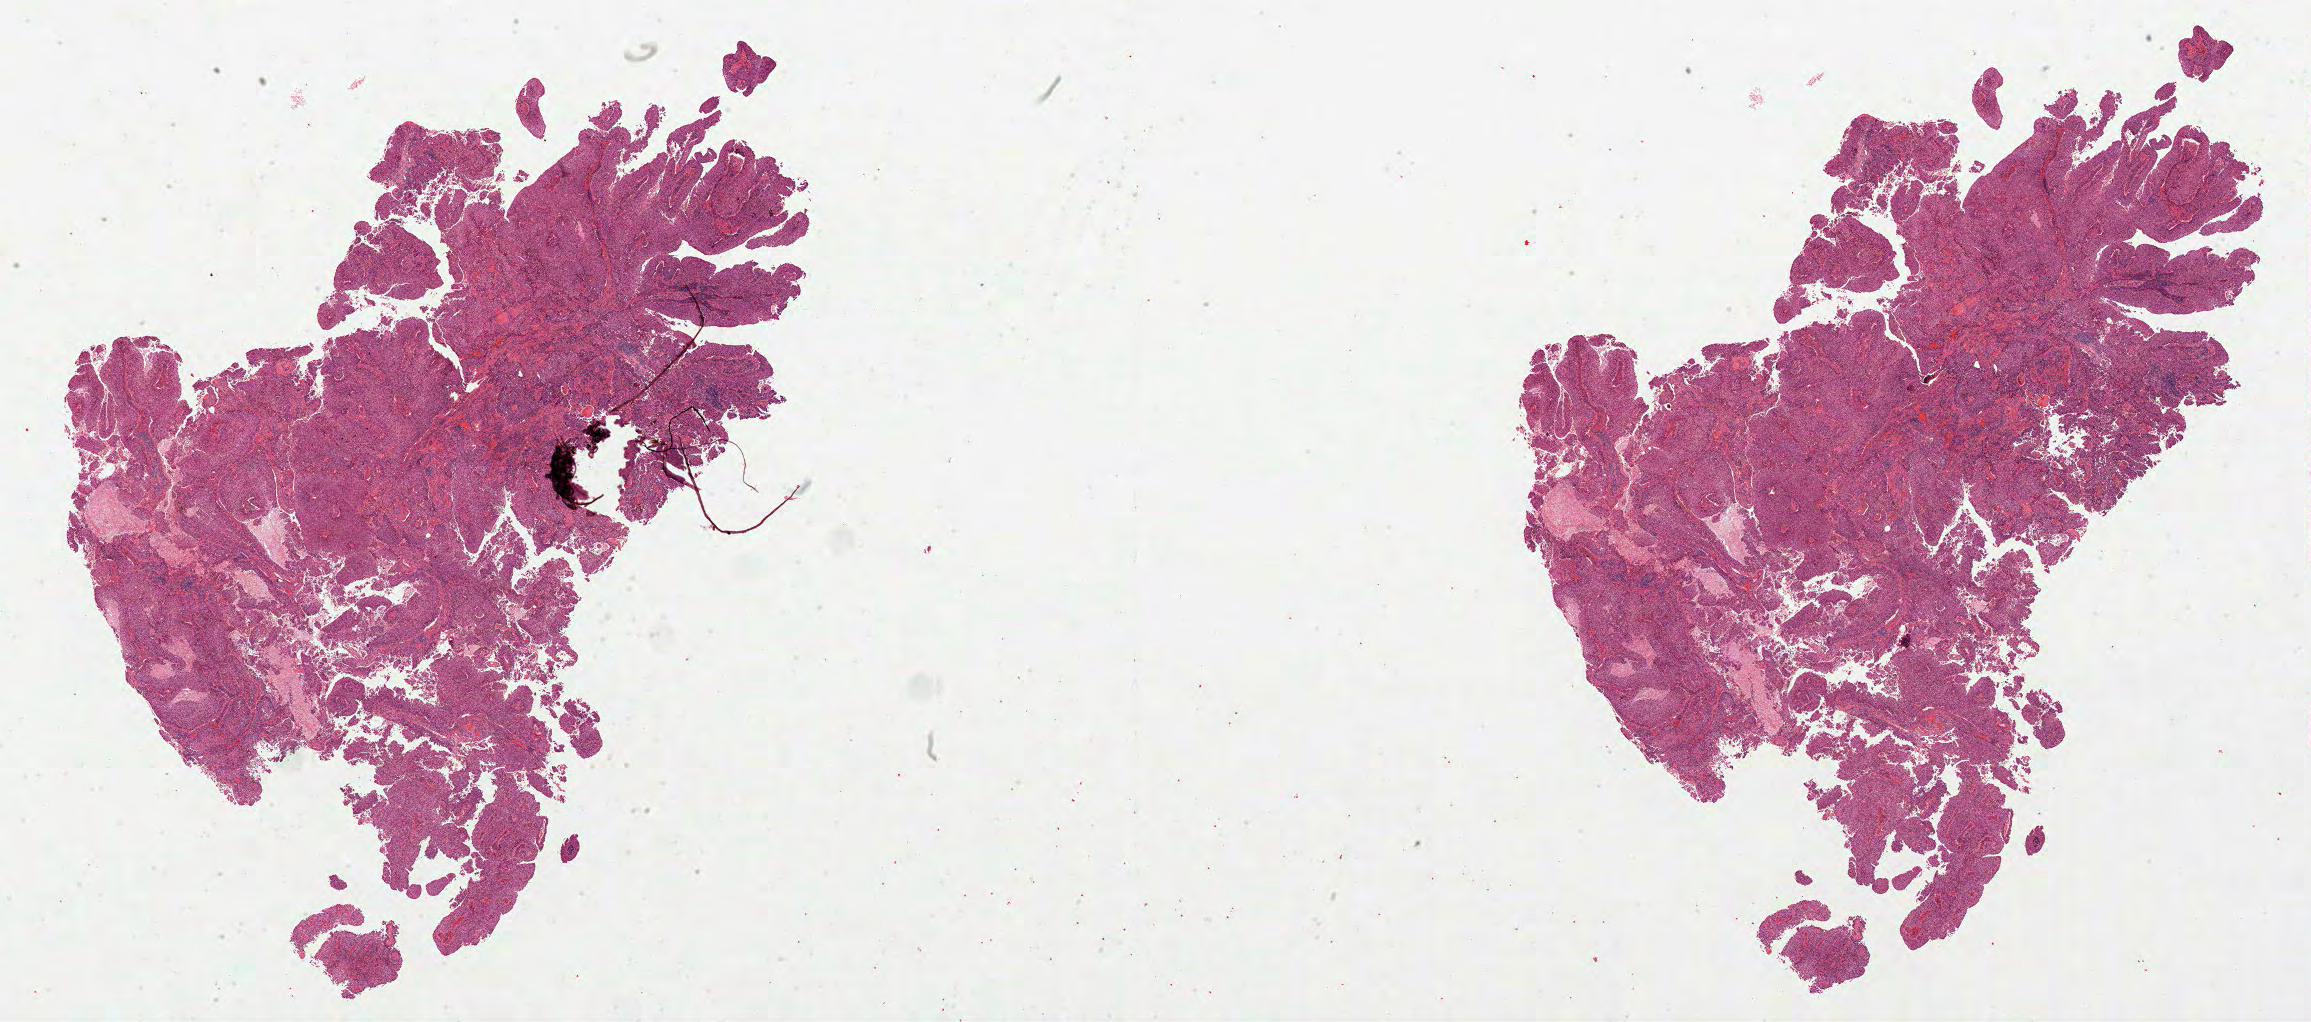
Digitized H&E-stained tissue section (whole slide) — low-resolution overview of the scanned area, about 37.0 x 16.4 mm (slide scanned at 20x), FFPE section, sample: primary tumour, kidney. Female patient.
TNM: T3 NX M0. Pathologic diagnosis: Papillary adenocarcinoma, NOS. AJCC pathologic stage: III (7th edition).